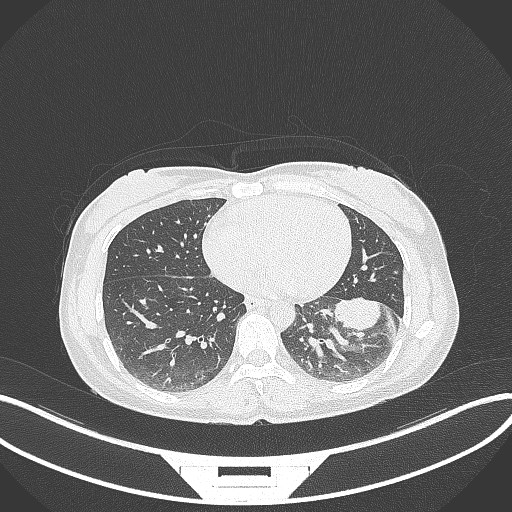
Chest CT, one axial slice. Slice 21 of 244 in the series (ordered by position). Lung window (W 1500 / L -600 HU). 512 × 512 image matrix, field of view 400 × 400 mm. Female patient, age 41 years. Case-level facts recorded for this patient, not image findings: clinical TNM (as recorded): T2a N3 M1b.
Annotated regions visible in this slice (bounding box drawn by a radiologist):
- lung tumour (recorded histology: adenocarcinoma): bounding box [x1, y1, x2, y2] px = [333, 296, 393, 336]